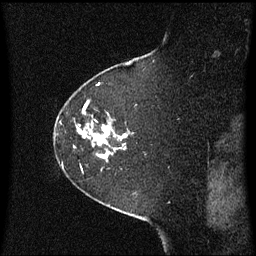
Breast MRI (dynamic contrast-enhanced), one sagittal slice; dynamic contrast-enhanced series, image 2 of 3 at this slice position (ordered by acquisition); 1.5 T; TE 4.2 ms, TR 8.4 ms; 2 mm slice thickness; 256 × 256 image matrix, field of view 210 × 210 mm. Patient: female, 60 years. From the clinical record (not read from this slice): setting: breast cancer imaged before/during neoadjuvant chemotherapy; receptor status: triple-negative.
Annotated regions visible in this slice (semi-automatic segmentation, software-assisted and operator-edited):
- analysis volume of interest (the breast-tissue region the enhancement analysis was run in; not a lesion): bounding box (x1, y1, x2, y2) in pixels: (55, 99, 136, 171)
- tumour enhancement mask (voxels above the 70 % enhancement threshold inside the analysis volume of interest): (80, 129, 112, 158)